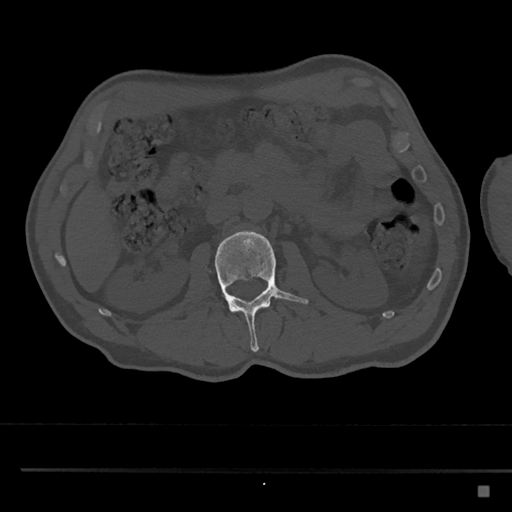
CT including the spine, one axial slice. Slice 756 of 797 in the series (ordered by position). Reconstruction kernel Br40s/3. 120 kVp. Bone window (W 1800 / L 400 HU). 0.5 mm slice thickness. 512 × 512 image matrix, field of view 391 × 391 mm. Male patient, age 59 years. From the clinical record (not read from this slice): primary cancer: prostate.
Structures marked on this image (semi-automatic segmentation, software-assisted and operator-edited):
- L2 vertebra: bounding box <206,229,309,352> (left, top, right, bottom; pixels)